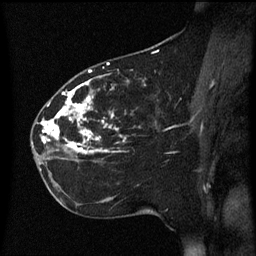
Breast MRI (dynamic contrast-enhanced), one sagittal slice. Slice 30 of 60 in the series (ordered by position). Dynamic contrast-enhanced series, image 2 of 3 at this slice position (ordered by acquisition). 1.5 T. TE 4.2 ms, TR 8.4 ms. 2.2 mm slice thickness. 256 × 256 image matrix, field of view 200 × 200 mm. Patient: female, 35 years. From the clinical record (not read from this slice): setting: breast cancer imaged before/during neoadjuvant chemotherapy; receptor status: HER2-positive.
Structures marked on this image (semi-automatic segmentation, software-assisted and operator-edited):
- analysis volume of interest (the breast-tissue region the enhancement analysis was run in; not a lesion): box from (x=32, y=78) to (x=170, y=163) px
- tumour enhancement mask (voxels above the 70 % enhancement threshold inside the analysis volume of interest): (x=42, y=80)–(x=119, y=155)